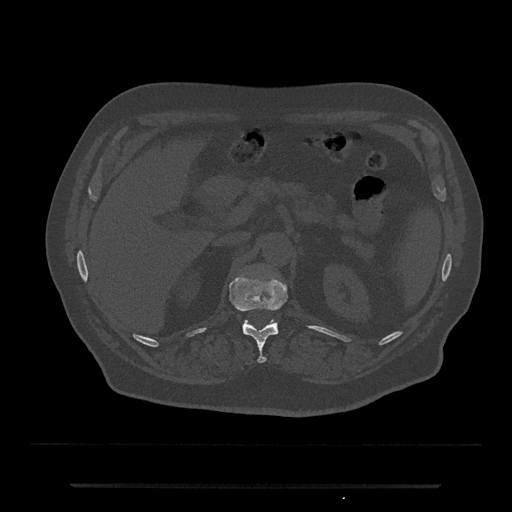
CT including the spine, one axial slice; slice 583 of 797 in the series (ordered by position); reconstruction kernel Br40s/3; bone window (W 1800 / L 400 HU); 0.5 mm slice thickness; 512 × 512 image matrix, field of view 434 × 434 mm. Patient: male, 80 years. Case-level facts recorded for this patient, not image findings: primary cancer: prostate; vertebrae with lytic lesions (as recorded): L1, T11.
Annotated regions visible in this slice (semi-automatic segmentation, software-assisted and operator-edited):
- T12 vertebra: bounding box [x1, y1, x2, y2] px = [229, 275, 288, 363]